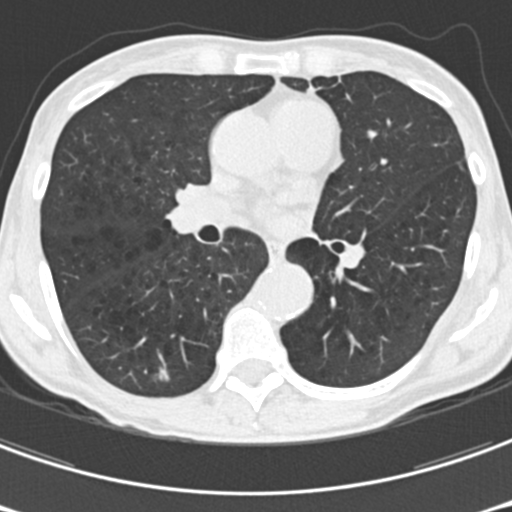
Low-dose screening chest CT, one axial slice. Position 95 of 176 along the scan axis. Reconstruction kernel B30f. 120 kVp. Lung window (W 1500 / L -600 HU). 2 mm slice thickness. 512 × 512 image matrix, field of view 277 × 277 mm.
Structures marked on this image (outlined manually by an expert reader):
- lesion 2 (nodule, upper lobe of right lung): bounding box [x1, y1, x2, y2] px = [157, 370, 168, 381]